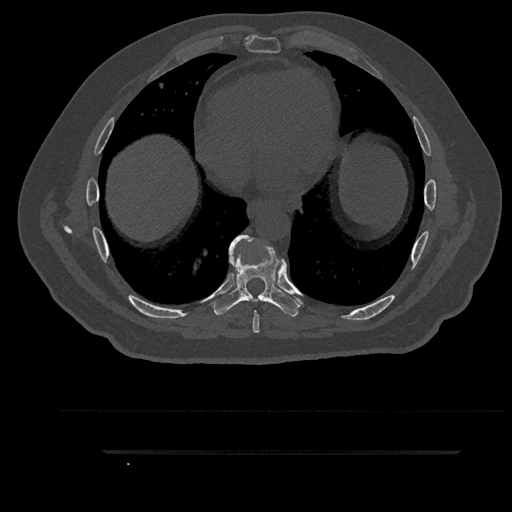
CT including the spine, one axial slice. Position 492 of 797 along the scan axis. Reconstruction kernel Br40s/3. Bone window (W 1800 / L 400 HU). 0.5 mm slice thickness. 512 × 512 image matrix. Patient: male, 63 years. From the clinical record (not read from this slice): primary cancer: renal.
Outlined on this slice (semi-automatically segmented with operator editing):
- T7 vertebra: box from (x=238, y=241) to (x=260, y=333) px
- T8 vertebra: (x=211, y=235)–(x=301, y=317)